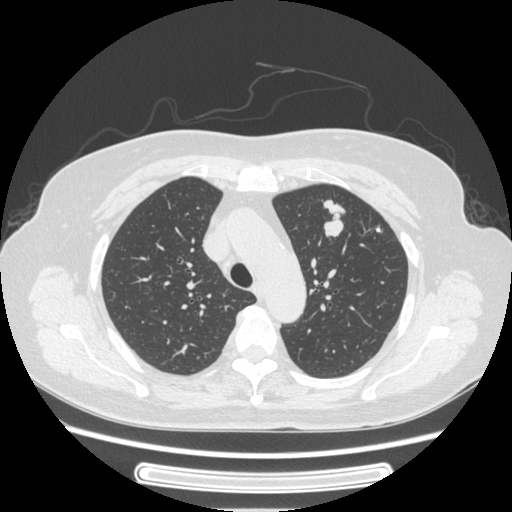
Chest CT, one axial slice; slice 176 of 227 in the series (ordered by position); lung window (W 1500 / L -600 HU); 1.25 mm slice thickness; 512 × 512 image matrix, field of view 363 × 363 mm. Patient: female, 77 years. Case-level facts recorded for this patient, not image findings: clinical TNM (as recorded): T1c N3 M0.
Outlined on this slice (bounding box drawn by a radiologist):
- lung tumour (recorded histology: adenocarcinoma): box from (x=314, y=193) to (x=352, y=250) px